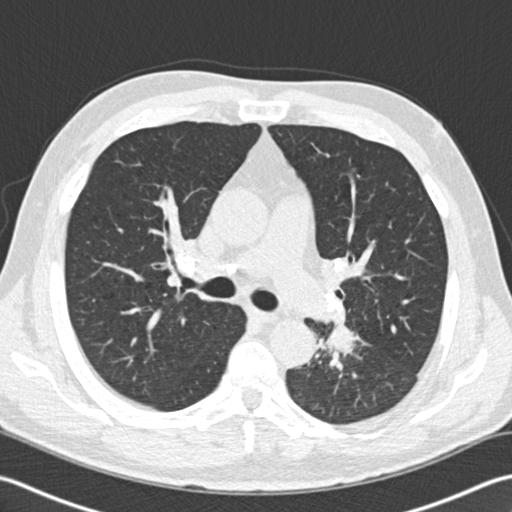
Low-dose screening chest CT, one axial slice. Slice 109 of 170 in the series (ordered by position). Reconstruction kernel B30f. 120 kVp. Lung window (W 1500 / L -600 HU). 512 × 512 image matrix, field of view 350 × 350 mm.
Structures marked on this image (outlined manually by an expert reader):
- lesion 1 (tumor, lower lobe of left lung): bounding box <326,324,358,356> (left, top, right, bottom; pixels)